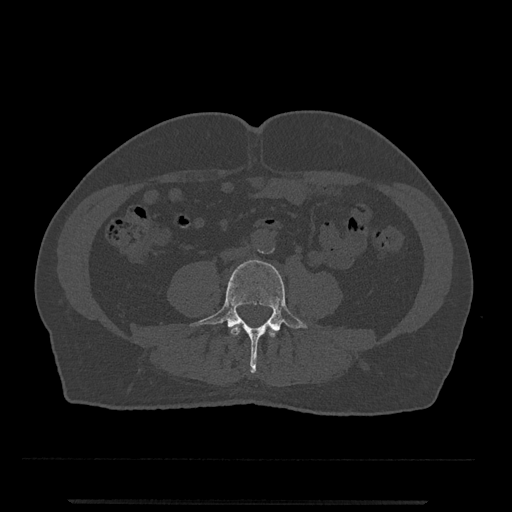
CT including the spine, one axial slice; reconstruction kernel Br40s/3; 120 kVp; bone window (W 1800 / L 400 HU); 512 × 512 image matrix, field of view 419 × 419 mm. Male patient, age 63 years. Case-level facts recorded for this patient, not image findings: primary cancer: prostate.
Outlined on this slice (semi-automatically segmented with operator editing):
- L3 vertebra: box from (x=230, y=325) to (x=277, y=337) px
- L4 vertebra: (x=189, y=259)–(x=308, y=372)